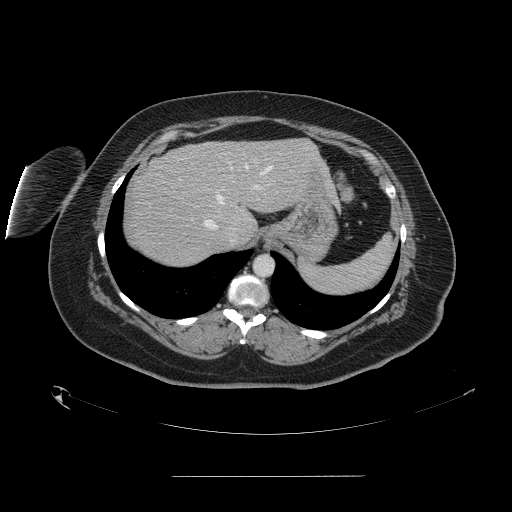
Contrast-enhanced abdominal CT, one axial slice; position 122 of 164 along the scan axis; 120 kVp; intravenous contrast given; soft-tissue window (W 400 / L 40 HU); 2.5 mm slice thickness; 512 × 512 image matrix, field of view 495 × 495 mm. Female patient, age 52 years. Case-level facts recorded for this patient, not image findings: diagnosis: colorectal cancer liver metastases, imaged before liver resection; multiple liver metastases: yes; largest metastasis: 3.5 cm; chemotherapy before resection: no.
Annotated regions visible in this slice (outlined manually by an expert reader):
- hepatic veins: bounding box <204,165,272,242> (left, top, right, bottom; pixels)
- liver: <124,139,321,267>
- planned liver remnant (the part of the liver to remain after resection): <170,139,318,224>
- portal vein (with intrahepatic branches): <179,179,259,189>